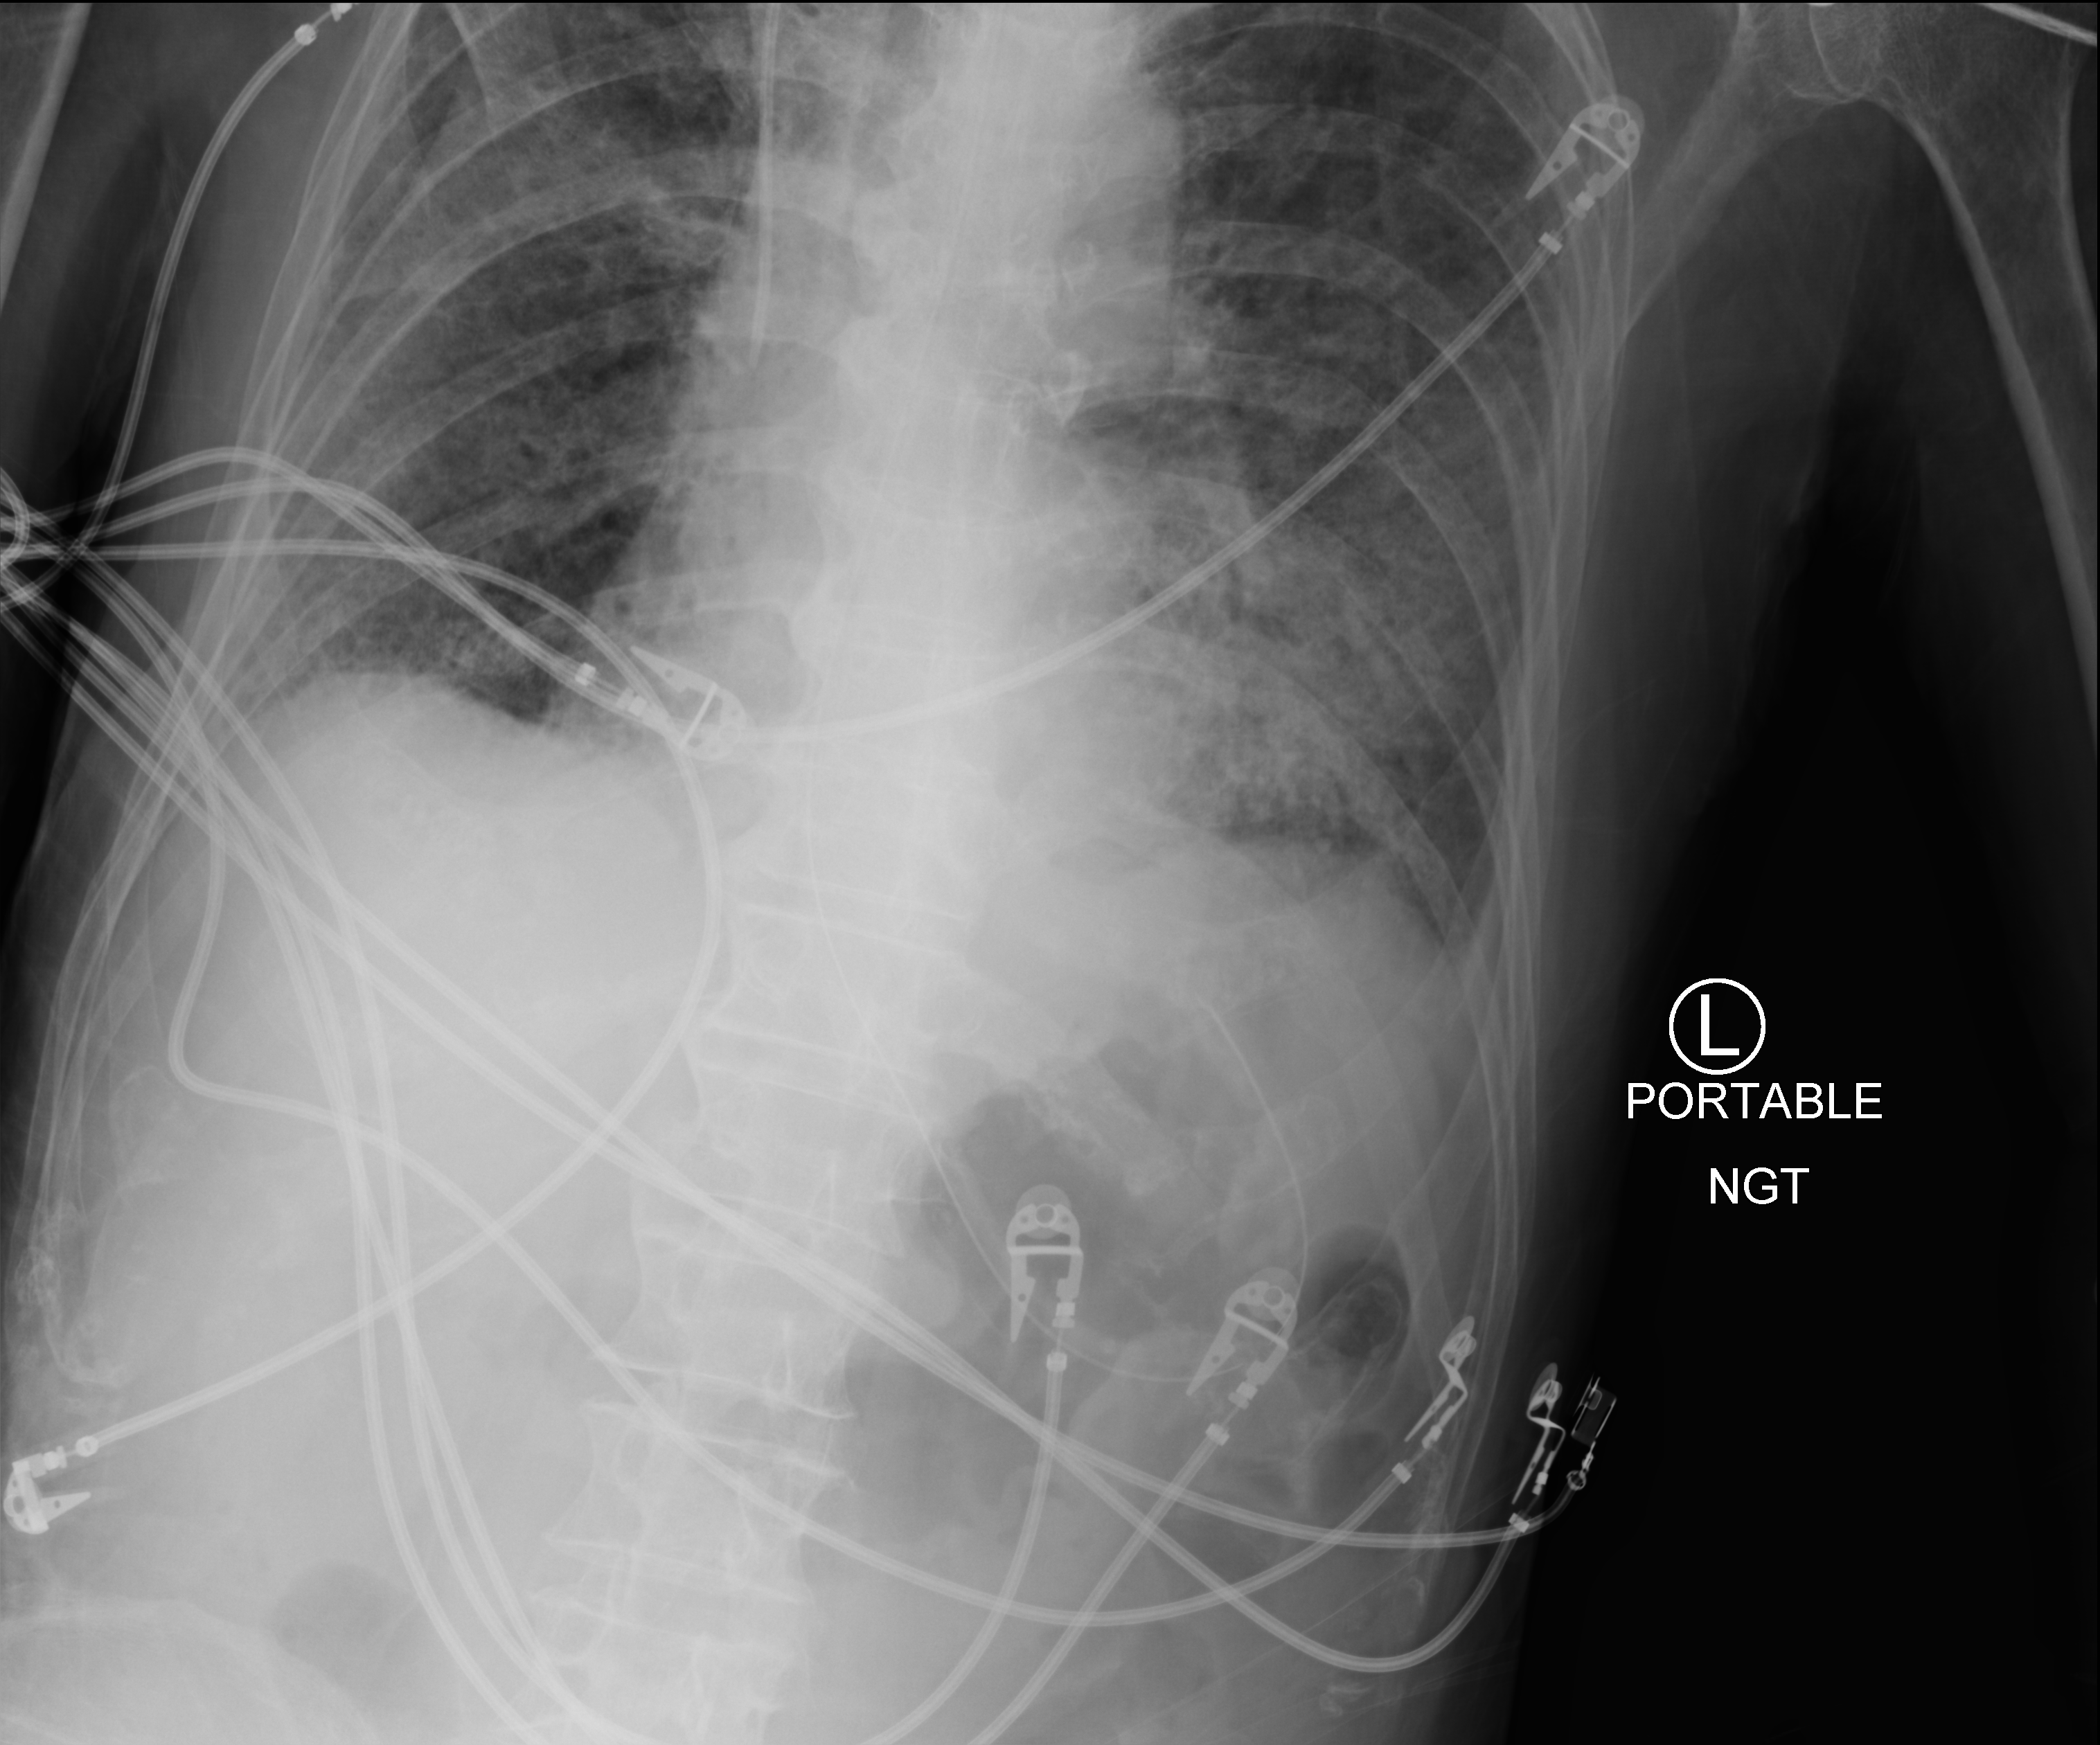
Chest X-ray (portable), anteroposterior (AP) projection. Male patient hospitalised with COVID-19, age 60–74 years.
Hospital-stay facts (about this admission, not read from this image; timing relative to this image not recorded): admitted to intensive care during this hospital stay: yes.